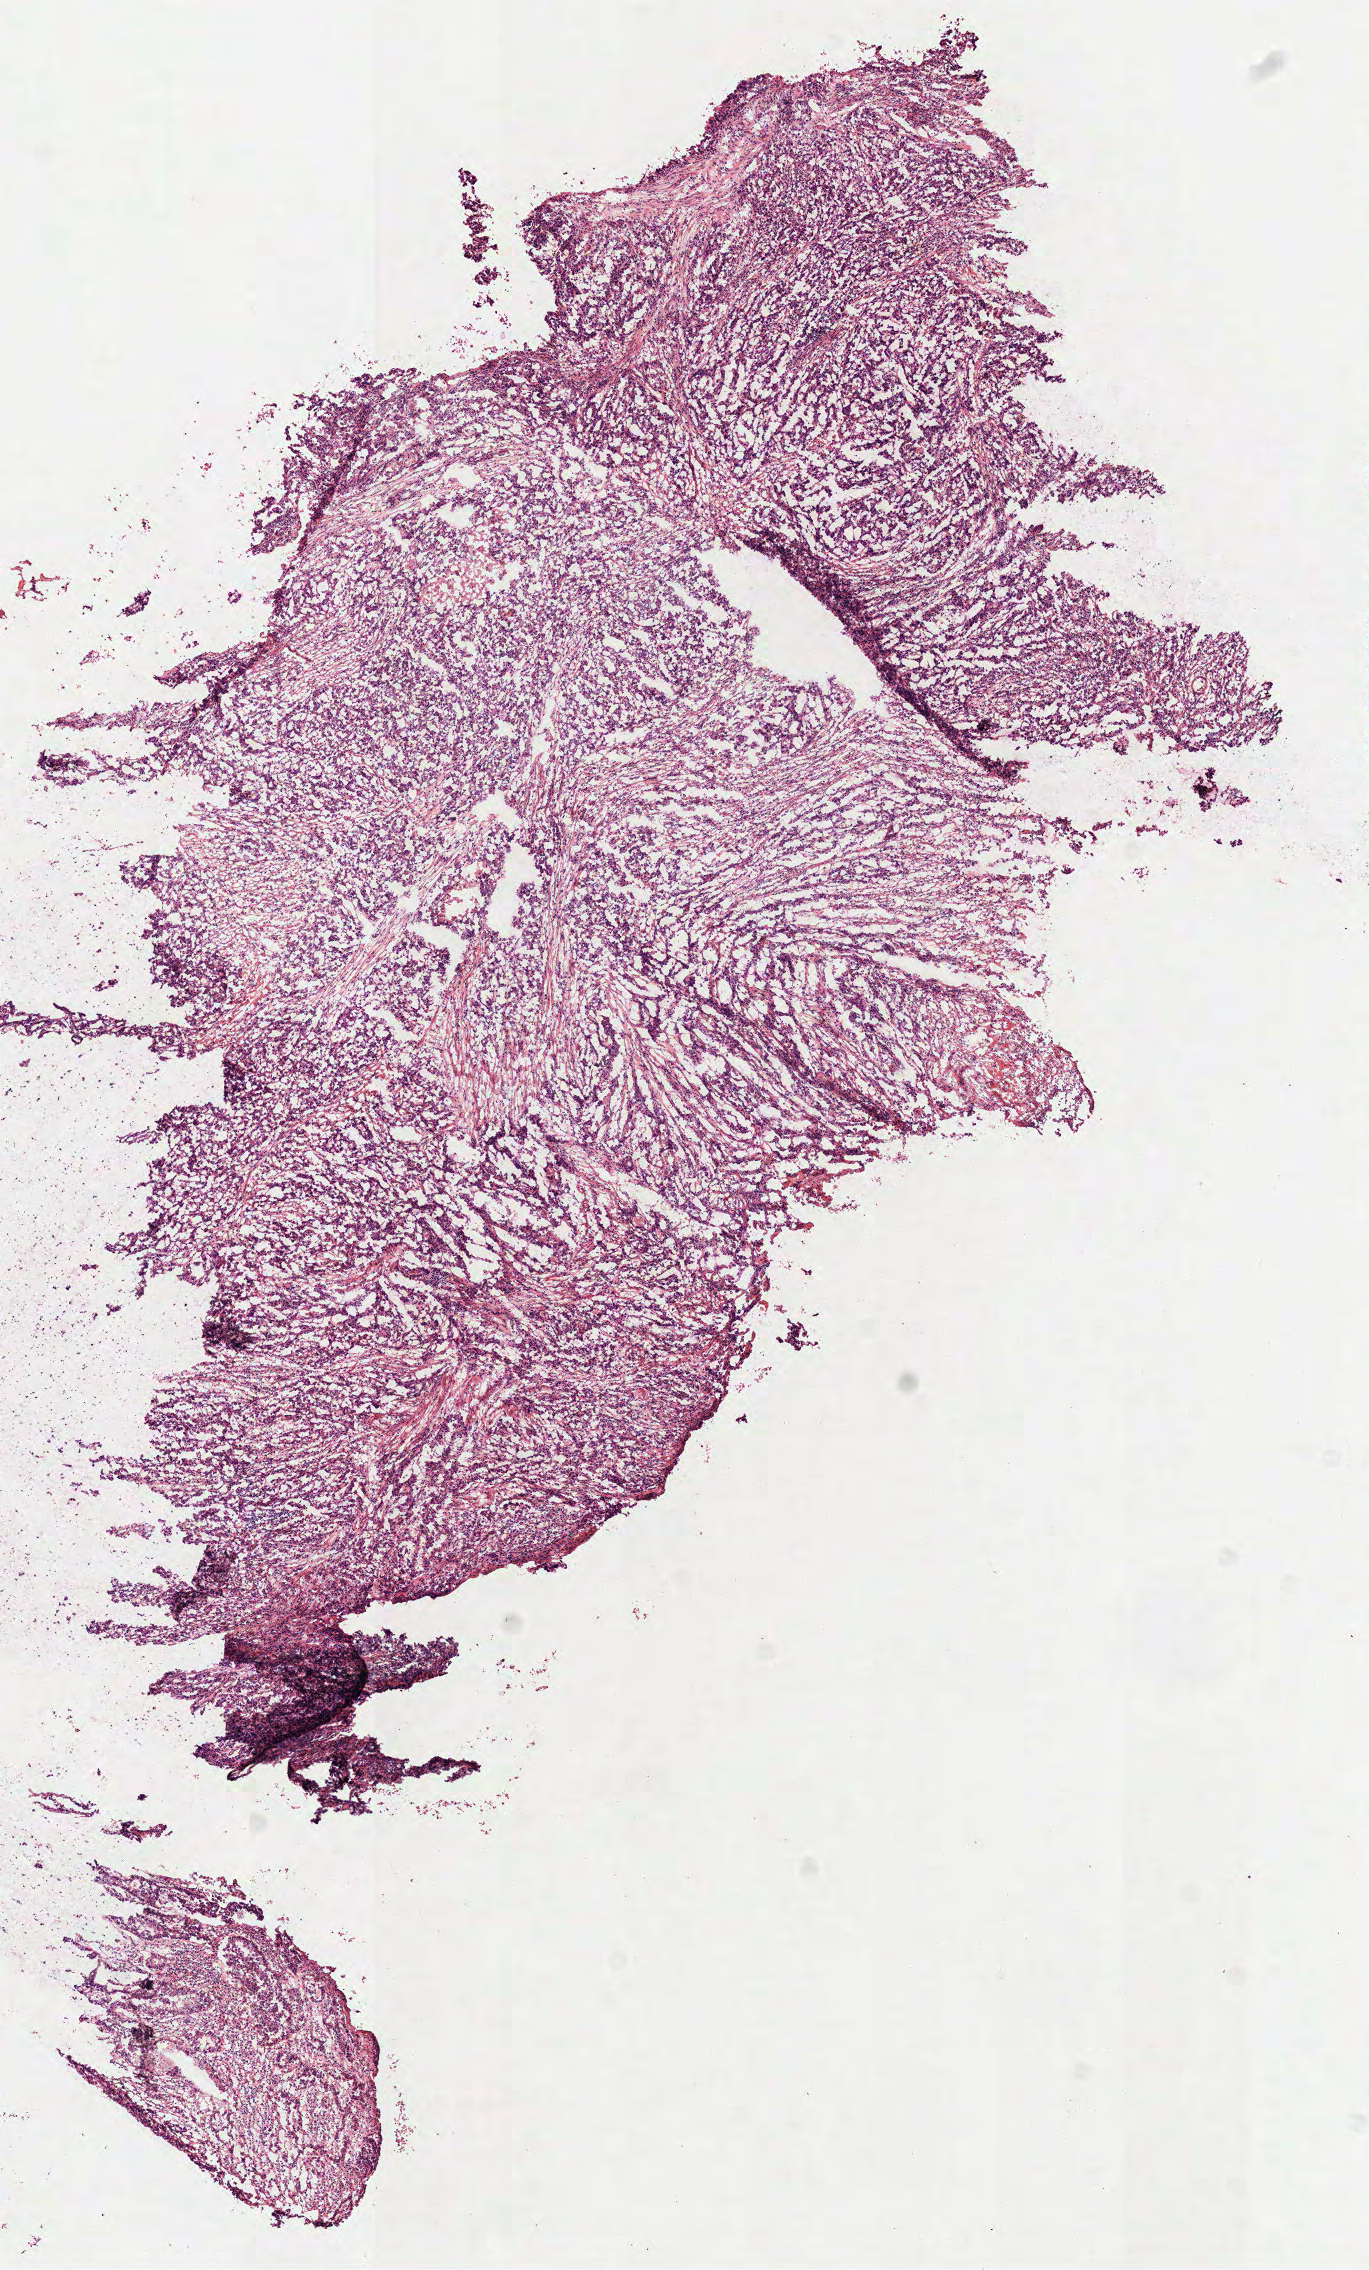
H&E whole-slide image, a low-resolution overview of the entire scanned area, about 5.5 x 9.2 mm (from a 40x scan). Frozen section from the top of the tissue portion. Sample: primary tumour, stomach. Female patient; age at initial diagnosis 73 years. Histologic grade: G3 (poorly differentiated). Slide review estimates, as recorded: tumour cells 90%, tumour nuclei 70%, normal cells 0%, stromal cells 10%, necrosis 0%.
Pathologic diagnosis: Adenocarcinoma, intestinal type (fundus of stomach). Lymph nodes positive (case pathology): 2 of 2 examined. AJCC pathologic stage: IIIA (6th edition). TNM: T3 N1 M0.